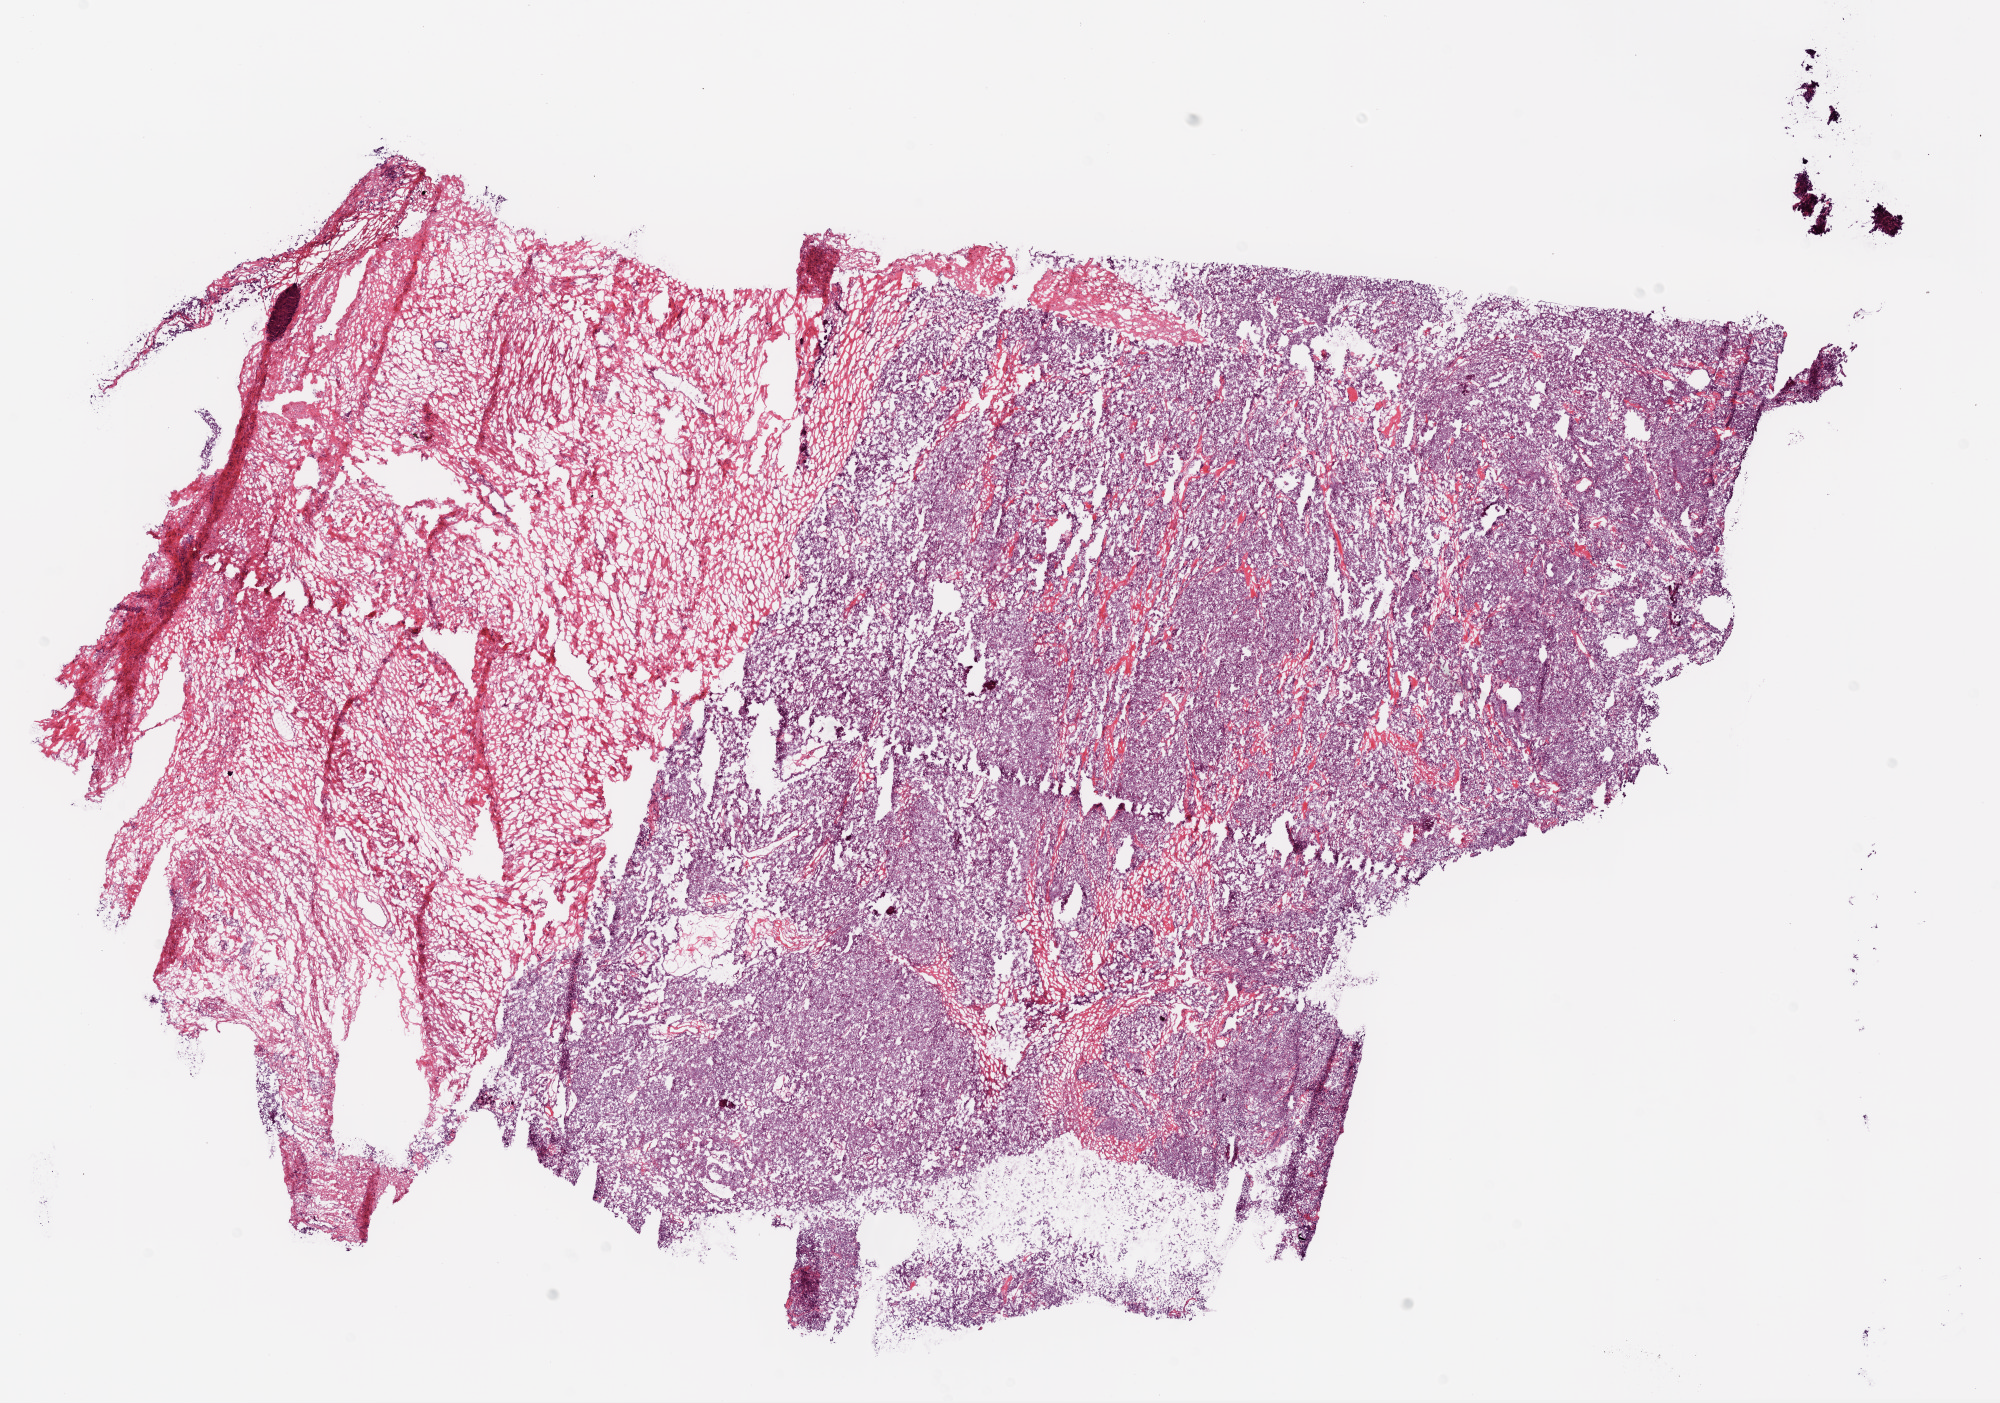
Hematoxylin and eosin (H&E) stained whole-slide image — a low-resolution overview of the entire scanned area, about 16.0 x 11.3 mm (slide scanned at 20x); frozen section from the top of the tissue portion; ovary, primary tumour sample. Female patient; age at initial diagnosis 76 years.
Histologic diagnosis: Serous cystadenocarcinoma, NOS.